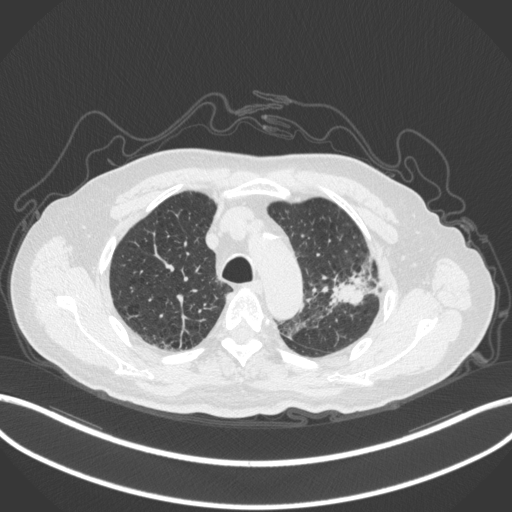
Chest CT, one axial slice; position 229 of 331 along the scan axis; 120 kVp; lung window (W 1500 / L -600 HU); 1 mm slice thickness; 512 × 512 image matrix, field of view 400 × 400 mm. Male patient, age 79 years. Case-level facts recorded for this patient, not image findings: clinical TNM (as recorded): T2a N1 M1; histopathological grade: G3.
Outlined on this slice (rectangle marked by the reading radiologist):
- lung tumour (recorded histology: adenocarcinoma): bounding box (x1, y1, x2, y2) in pixels: (330, 257, 379, 305)